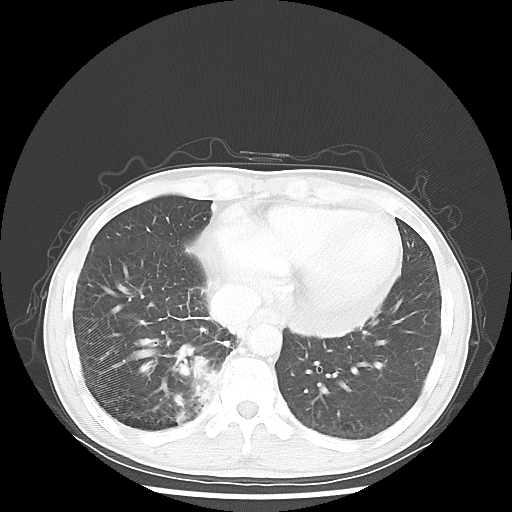
Chest CT, one axial slice. Position 14 of 58 along the scan axis. 100 kVp. Lung window (W 1500 / L -600 HU). 5 mm slice thickness. 512 × 512 image matrix, field of view 360 × 360 mm. Male patient, age 56 years. From the clinical record (not read from this slice): clinical TNM (as recorded): T2 N1 M1; histopathological grade: G1.
Structures marked on this image (rectangle marked by the reading radiologist):
- lung tumour (recorded histology: adenocarcinoma): bounding box [x1, y1, x2, y2] px = [184, 353, 219, 406]